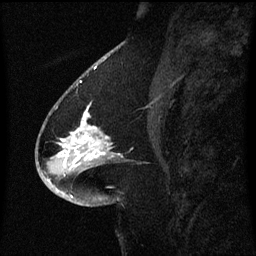
Breast MRI (dynamic contrast-enhanced), one sagittal slice; slice 27 of 60 in the series (ordered by position); dynamic contrast-enhanced series, image 2 of 3 at this slice position (ordered by acquisition); 1.5 T; TE 4.2 ms, TR 8.4 ms; 2 mm slice thickness; 256 × 256 image matrix, field of view 200 × 200 mm. Female patient, age 54 years. From the clinical record (not read from this slice): setting: breast cancer imaged before/during neoadjuvant chemotherapy; receptor status: HR-positive, HER2-negative.
Outlined on this slice (semi-automatically segmented with operator editing):
- analysis volume of interest (the breast-tissue region the enhancement analysis was run in; not a lesion): box from (x=46, y=100) to (x=123, y=171) px
- tumour enhancement mask (voxels above the 70 % enhancement threshold inside the analysis volume of interest): (x=62, y=106)–(x=101, y=149)